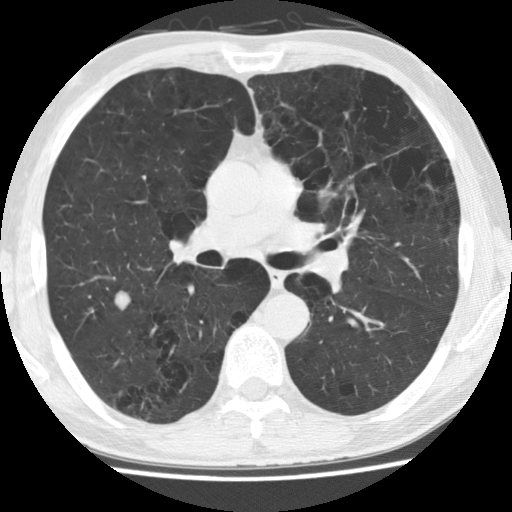
Low-dose screening chest CT, one axial slice. Slice 88 of 158 in the series (ordered by position). Lung window (W 1500 / L -600 HU). 2.5 mm slice thickness. 512 × 512 image matrix.
Structures marked on this image (outlined manually by an expert reader):
- lesion 1 (tumor, upper lobe of right lung): bounding box <115,291,130,310> (left, top, right, bottom; pixels)